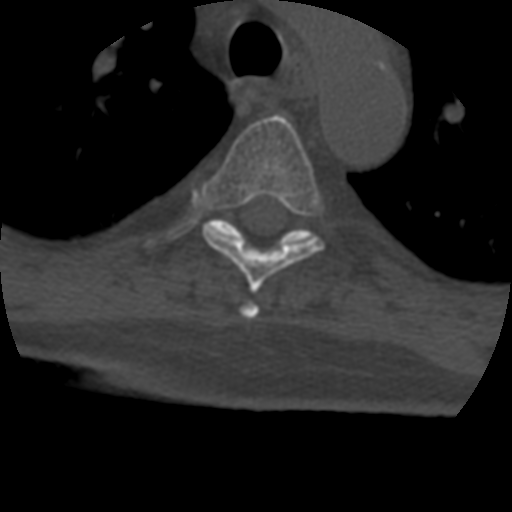
CT including the spine, one axial slice; slice 316 of 399 in the series (ordered by position); 120 kVp; bone window (W 1800 / L 400 HU); 1.25 mm slice thickness; 512 × 512 image matrix, field of view 160 × 160 mm. Patient age 69 years. From the clinical record (not read from this slice): primary cancer: prostate.
Structures marked on this image (semi-automatic segmentation, software-assisted and operator-edited):
- T4 vertebra: bounding box [x1, y1, x2, y2] px = [241, 302, 259, 319]
- T5 vertebra: [203, 116, 325, 294]
- T6 vertebra: [207, 219, 314, 244]